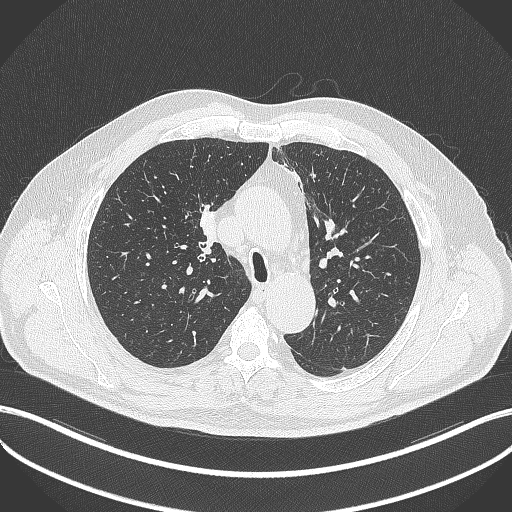
Chest CT, one axial slice; position 267 of 411 along the scan axis; reconstruction kernel B70f; lung window (W 1500 / L -600 HU); 1 mm slice thickness; 512 × 512 image matrix, field of view 400 × 400 mm. Male patient, age 60 years. Case-level facts recorded for this patient, not image findings: clinical TNM (as recorded): T1b N1 M0.
Structures marked on this image (rectangle marked by the reading radiologist):
- lung tumour (recorded histology: squamous cell carcinoma): bounding box [x1, y1, x2, y2] px = [194, 200, 220, 248]